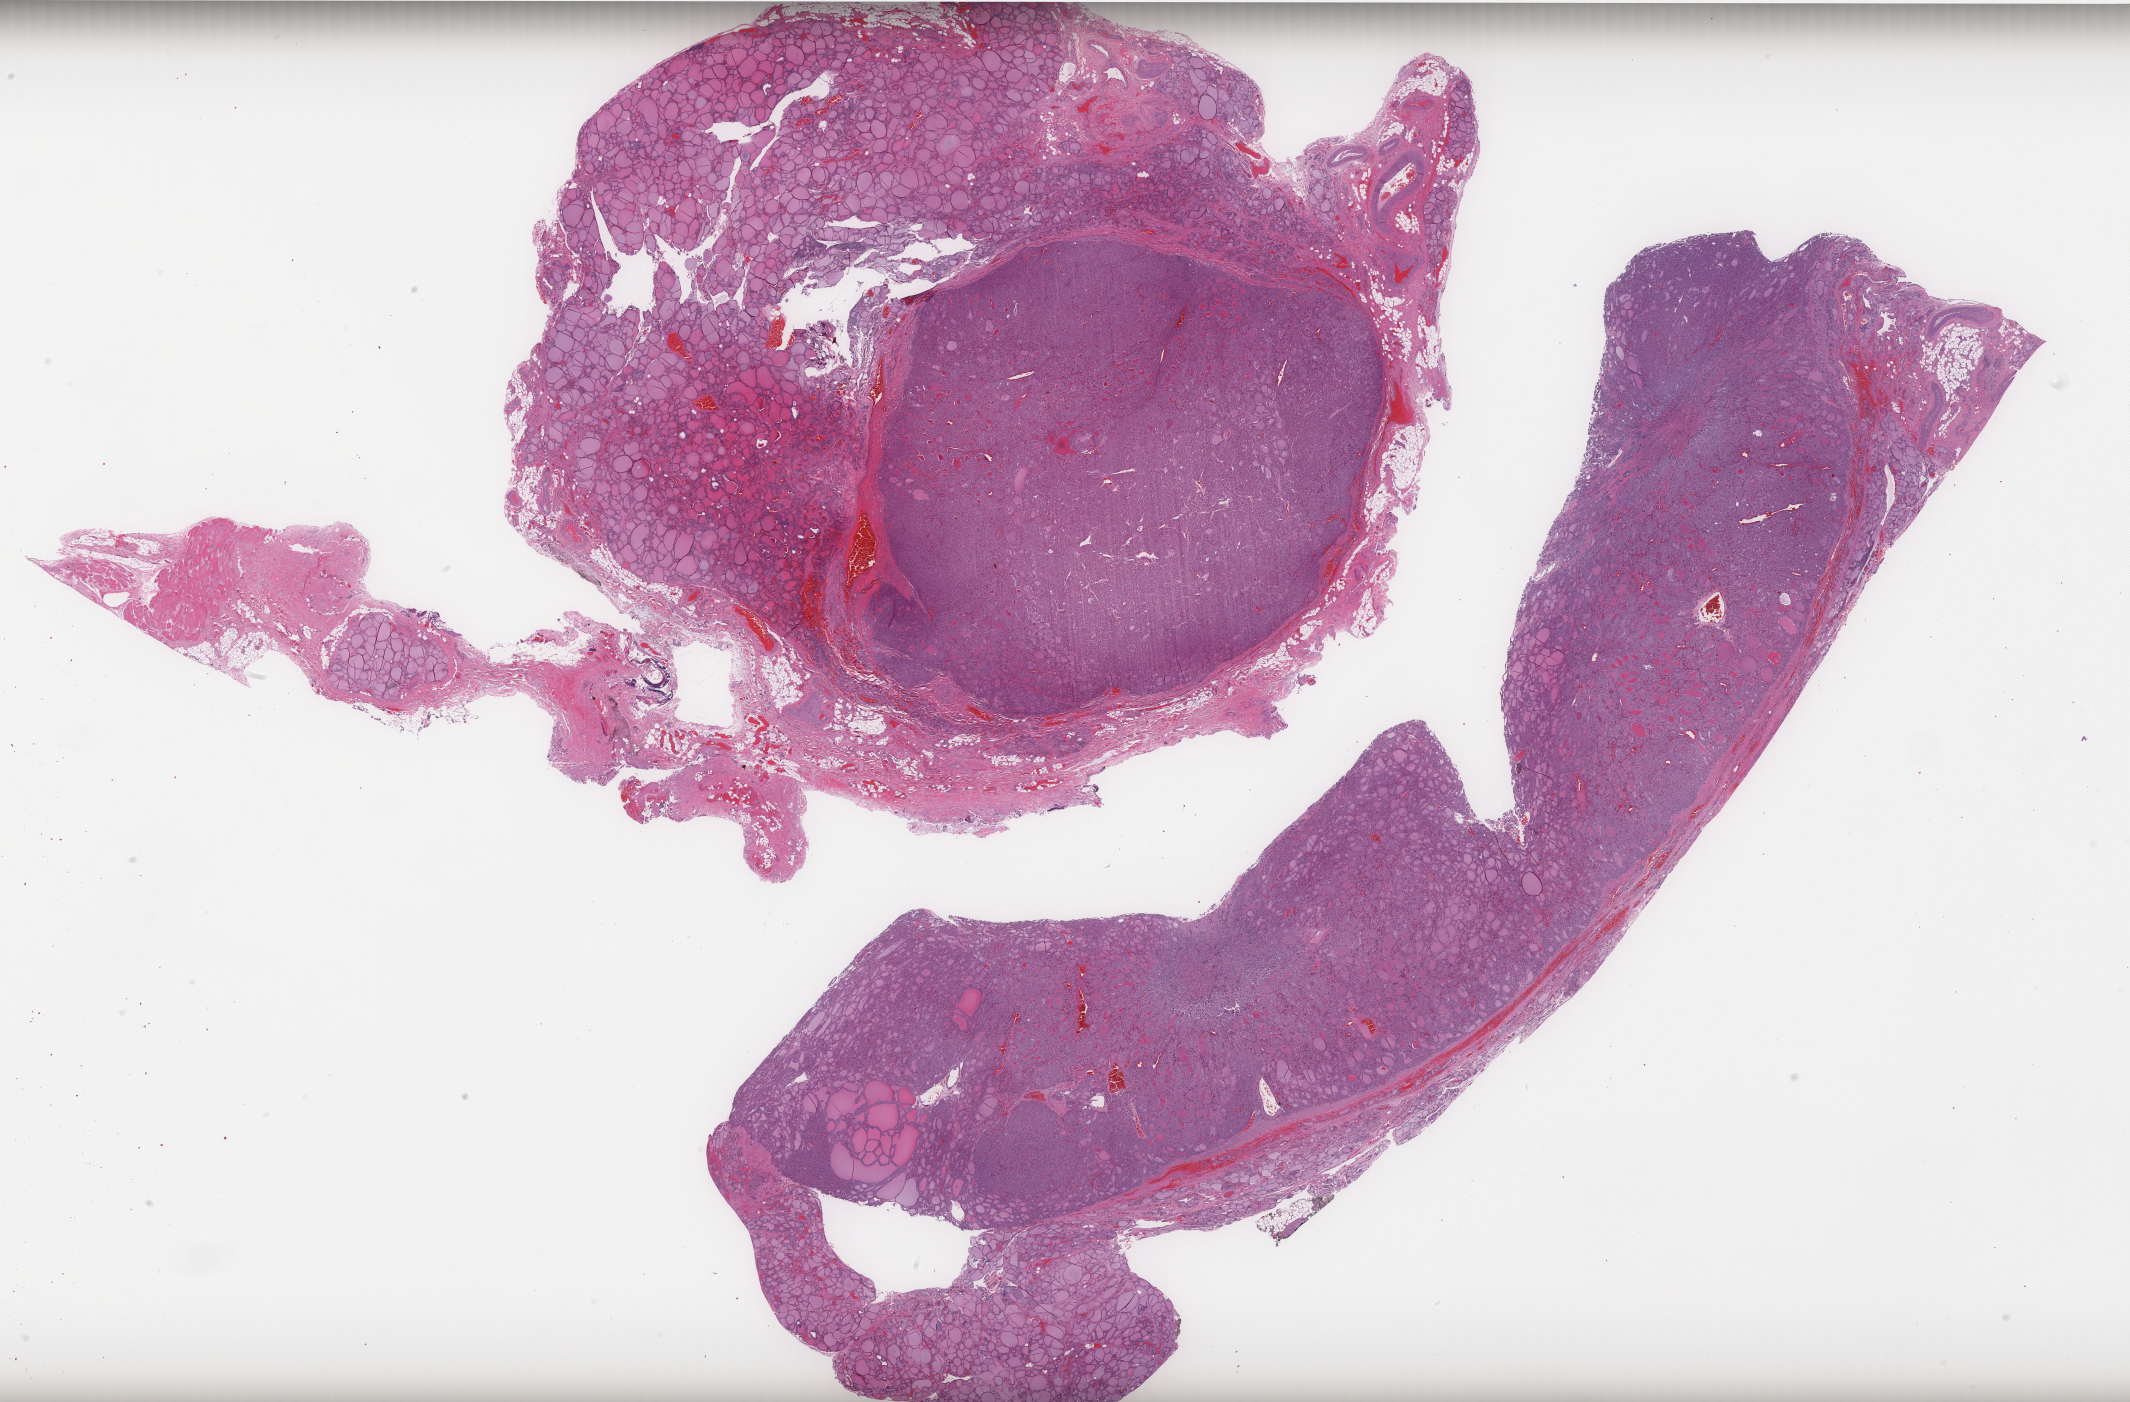
Digitized Hematoxylin and eosin (H&E) stained tissue section (whole slide), shown as a low-resolution overview of the whole scanned area (about 34.2 x 22.5 mm, slide scanned at 40x); FFPE section; thyroid, primary tumour sample. Male, age 62 years at initial diagnosis.
* pathologic diagnosis: Papillary carcinoma, follicular variant (thyroid gland)
* AJCC pathologic stage: I (7th edition)